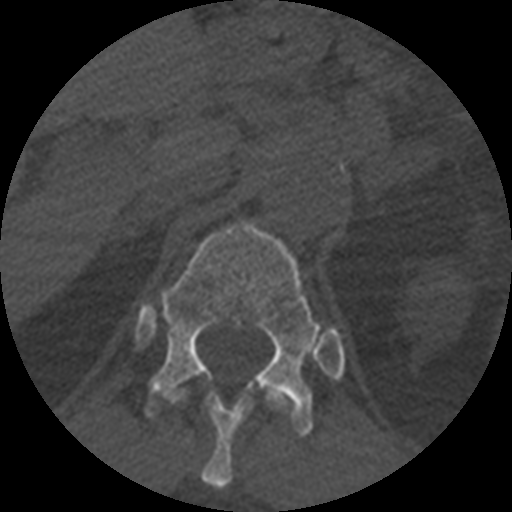
CT including the spine, one axial slice; position 393 of 399 along the scan axis; reconstruction kernel STANDARD; 120 kVp; bone window (W 1800 / L 400 HU); 1.25 mm slice thickness; 512 × 512 image matrix, field of view 160 × 160 mm. Patient age 71 years. Case-level facts recorded for this patient, not image findings: primary cancer: prostate.
Annotated regions visible in this slice (semi-automatic segmentation, software-assisted and operator-edited):
- T11 vertebra: bounding box (x1, y1, x2, y2) in pixels: (203, 391, 293, 489)
- T12 vertebra: (146, 222, 322, 436)